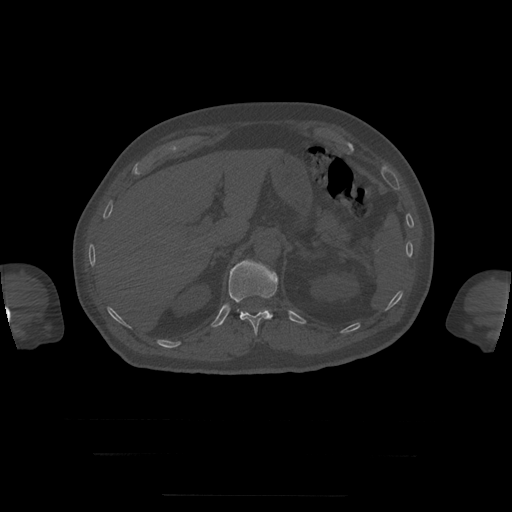
CT including the spine, one axial slice. Position 71 of 397 along the scan axis. Reconstruction kernel STANDARD. 120 kVp. Bone window (W 1800 / L 400 HU). 1.25 mm slice thickness. 512 × 512 image matrix. Patient age 73 years. From the clinical record (not read from this slice): primary cancer: prostate.
Structures marked on this image (semi-automatic segmentation, software-assisted and operator-edited):
- T12 vertebra: bounding box [x1, y1, x2, y2] px = [229, 260, 278, 335]